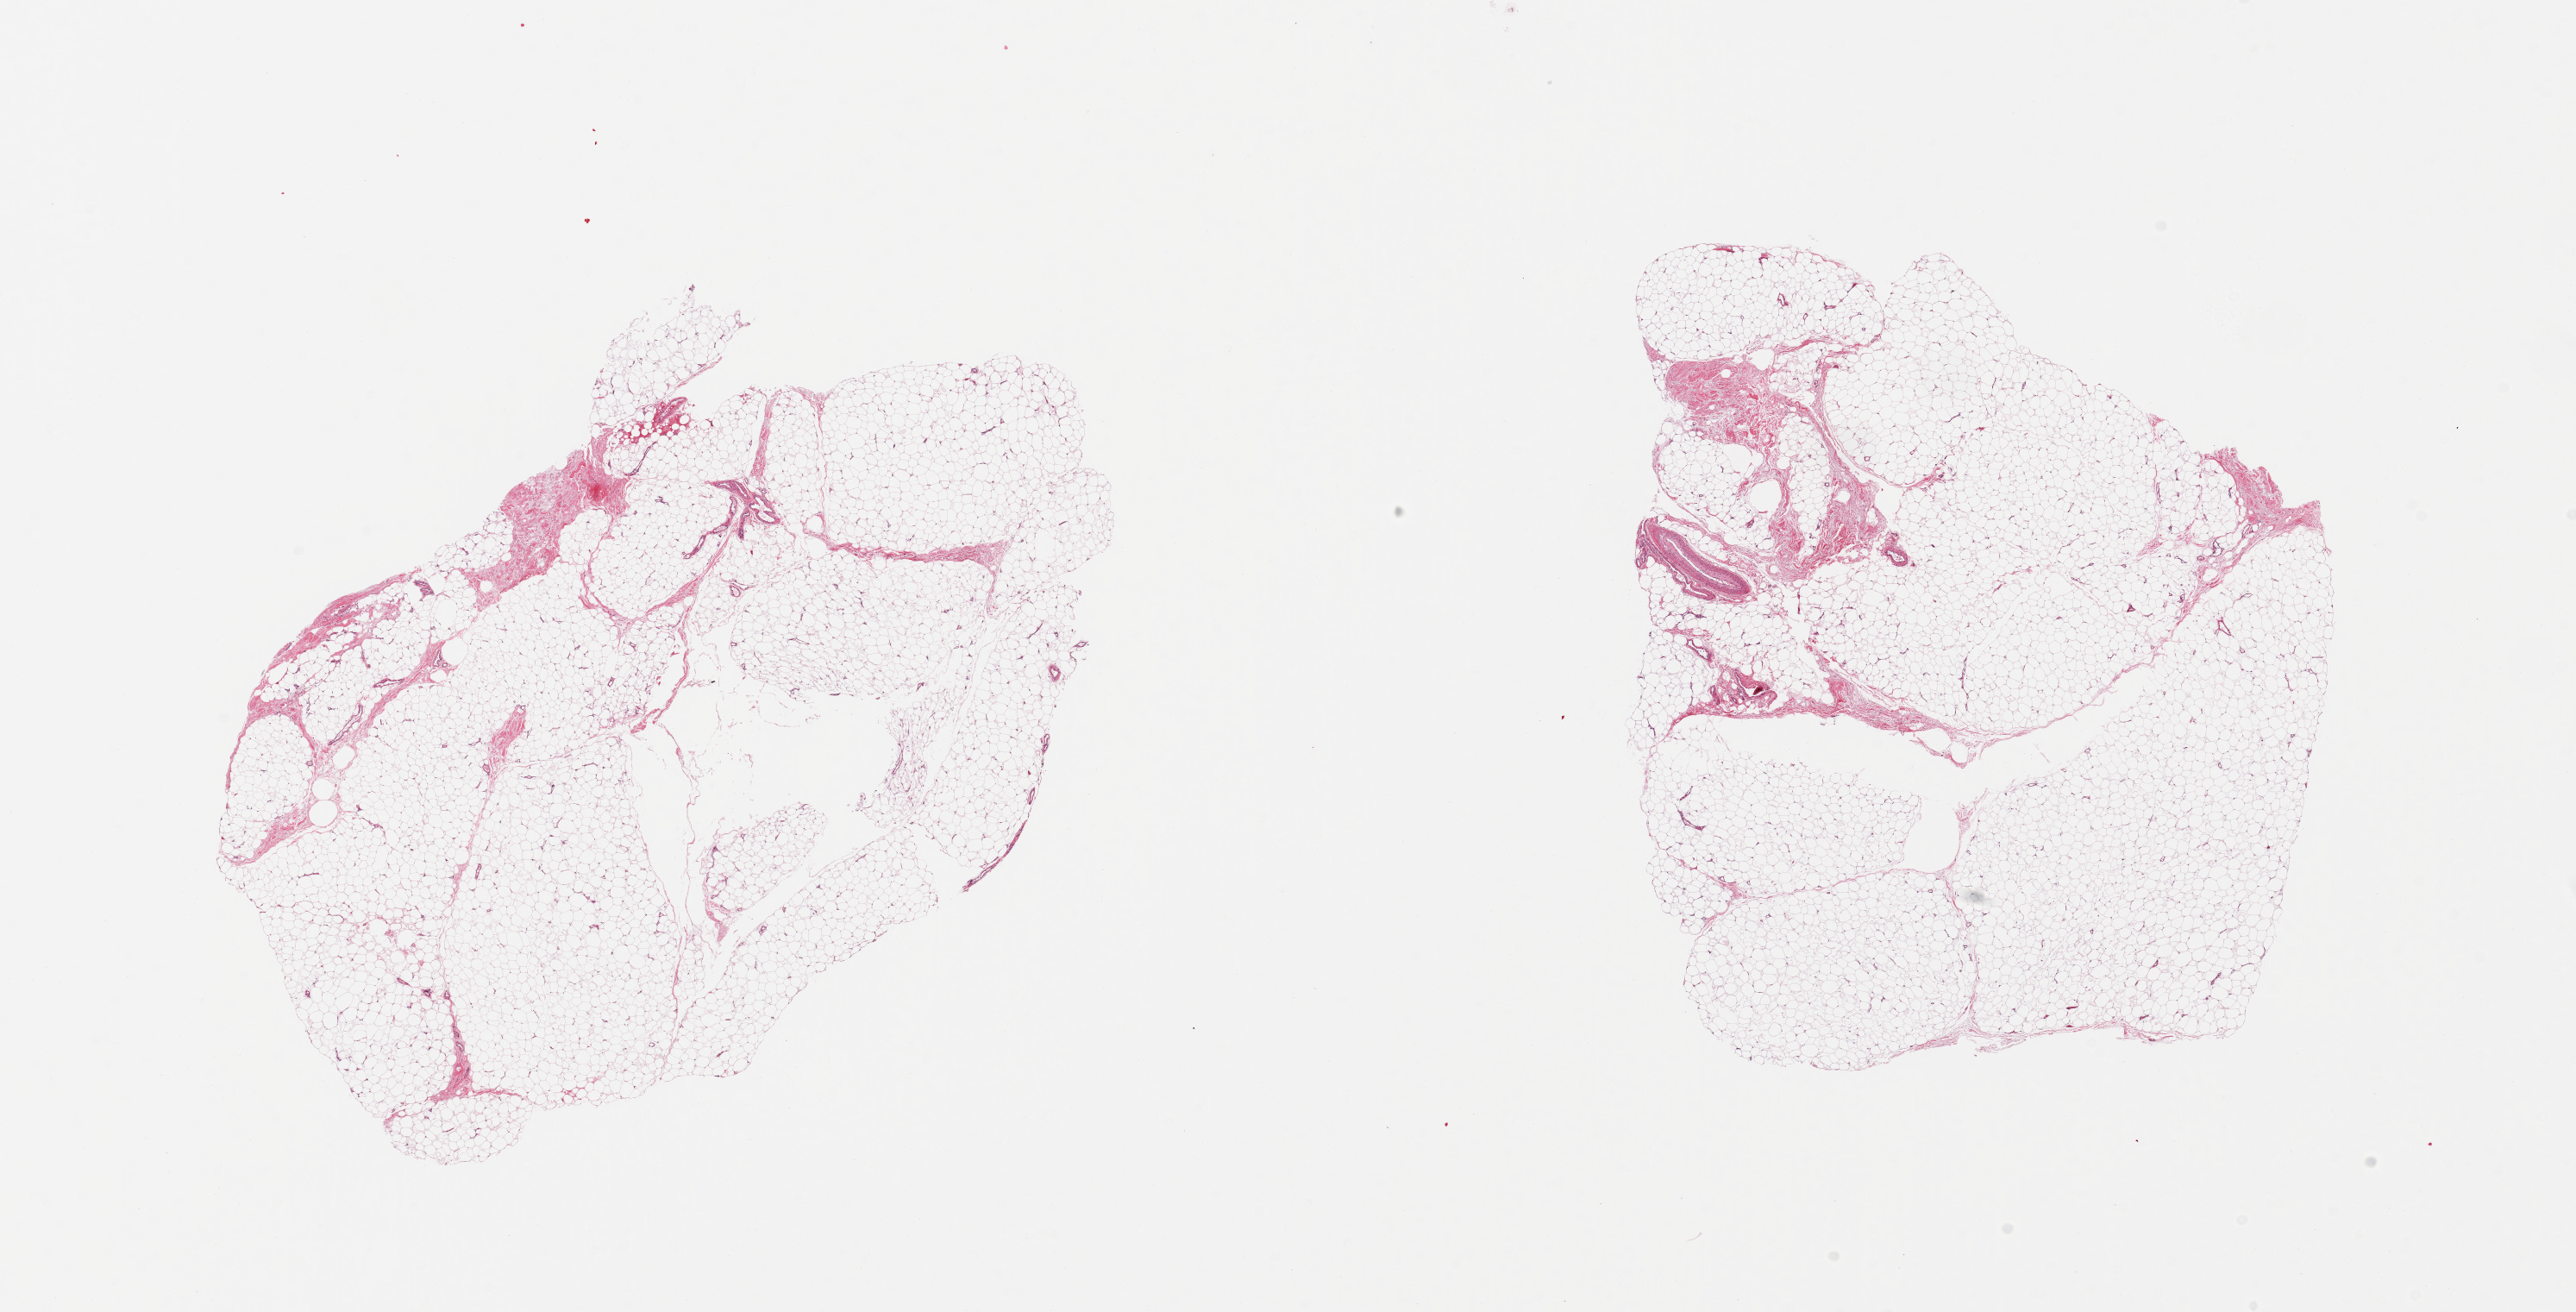
Digitized H&E-stained section, brightfield, whole scanned area (about 23.6 x 12.0 mm) shown as a low-resolution overview. PAXgene-fixed paraffin-embedded (PFPE) section. Target tissue: adipose tissue. Donor tissue sample. Male donor.
Review note (as recorded): 2 pieces; mature adipose tissue, up to ~10% fibrous tissue/vessels.